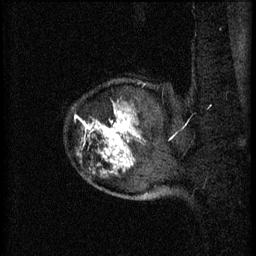
Breast MRI (dynamic contrast-enhanced), one sagittal slice; position 55 of 60 along the scan axis; 3 images stored at this slice position (order not interpretable as contrast timing); 1.5 T; TE 4.2 ms, TR 11 ms; 2 mm slice thickness; 256 × 256 image matrix, field of view 180 × 180 mm. Patient: female, 52 years.
Structures marked on this image (semi-automatically segmented with operator editing):
- analysis volume of interest (the breast-tissue region the enhancement analysis was run in; not a lesion): bounding box (x1, y1, x2, y2) in pixels: (83, 84, 146, 157)
- tumour enhancement mask (voxels above the 70 % enhancement threshold inside the analysis volume of interest): (87, 110, 134, 157)